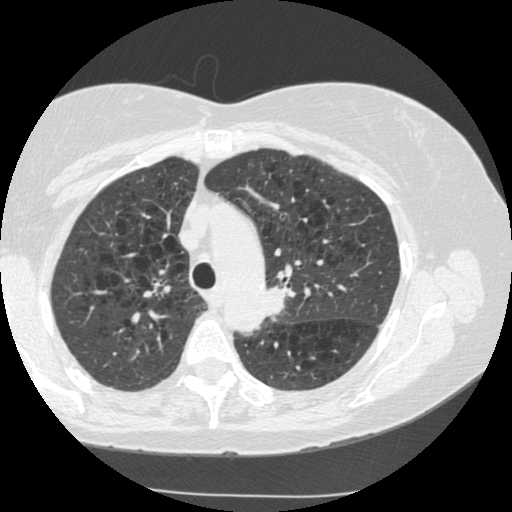
Low-dose screening chest CT, axial slice, second annual screen, lung window (W 1500 / L -600 HU), 1.25 mm slice thickness, standard (soft-tissue) reconstruction kernel (STANDARD), slice 189 of 249 in the series. Female, age 70 years at enrolment.
Expert reader's lesion annotation, bounding box [x1, y1, x2, y2] px = [244, 268, 311, 330]. The exam's reader record, not a measurement of the box and not confirmed to be the same lesion: non-calcified nodule or mass ≥4 mm, left upper lobe, 15 × 13 mm, spiculated (stellate) margins, soft tissue attenuation, pre-existing on the prior screen: yes; interval growth: yes. Official screen result: positive, other. Later outcome: lung cancer diagnosed 360 days after this screen (after the third annual screen) — neoplasm, malignant, left upper lobe, stage IIIB (AJCC 6th edition), 40 mm at pathology.